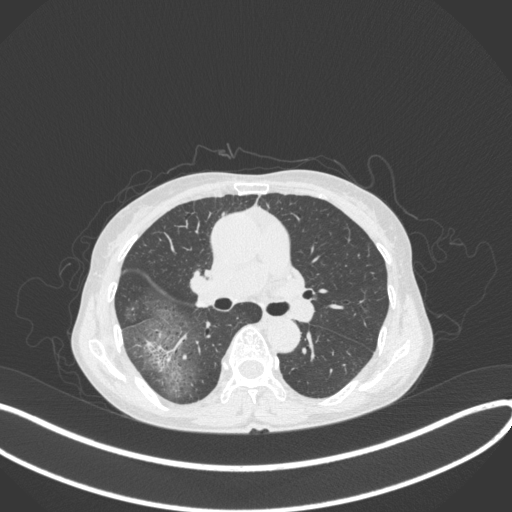
Chest CT, one axial slice; slice 233 of 379 in the series (ordered by position); reconstruction kernel B31f; 120 kVp; lung window (W 1500 / L -600 HU); 1 mm slice thickness; 512 × 512 image matrix, field of view 400 × 400 mm. Female patient, age 69 years. From the clinical record (not read from this slice): clinical TNM (as recorded): T1b N0 M0.
Structures marked on this image (bounding box drawn by a radiologist):
- lung tumour (recorded histology: adenocarcinoma): box from (x=141, y=323) to (x=192, y=373) px